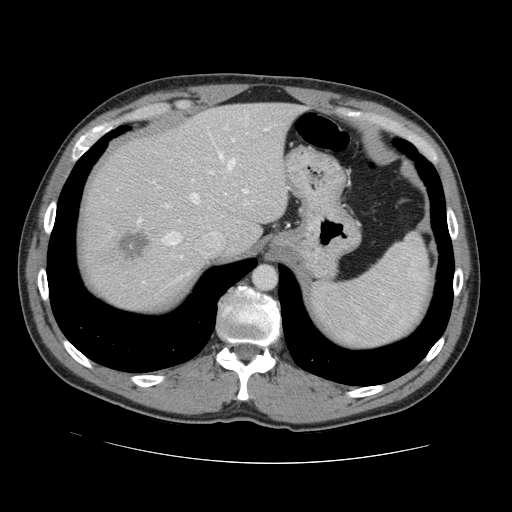
Contrast-enhanced abdominal CT, one axial slice; position 109 of 131 along the scan axis; intravenous contrast given; soft-tissue window (W 400 / L 40 HU); 2.5 mm slice thickness; 512 × 512 image matrix. Male patient, age 40 years. From the clinical record (not read from this slice): diagnosis: colorectal cancer liver metastases, imaged before liver resection; multiple liver metastases: yes; largest metastasis: 2.9 cm; chemotherapy before resection: yes.
Annotated regions visible in this slice (expert manual segmentation):
- hepatic veins: box from (x=162, y=153) to (x=236, y=245) px
- liver: (x=80, y=104)–(x=298, y=308)
- planned liver remnant (the part of the liver to remain after resection): (x=106, y=104)–(x=299, y=254)
- portal vein (with intrahepatic branches): (x=209, y=133)–(x=249, y=194)
- liver metastasis: (x=116, y=228)–(x=151, y=260)